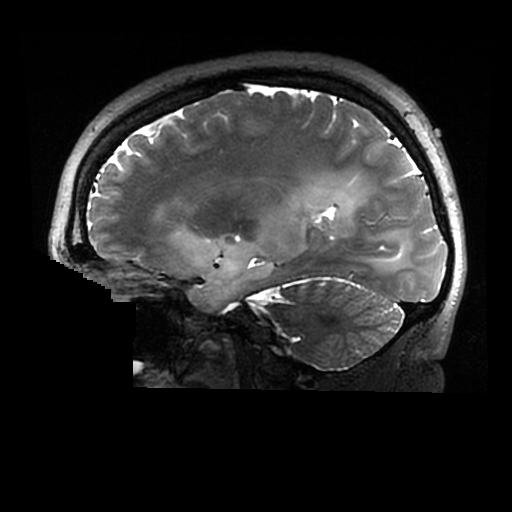
Brain MRI from a brain-tumour surgery series, one sagittal slice; position 185 of 320 along the scan axis; 0.6 mm slice thickness; 512 × 512 image matrix, field of view 240 × 240 mm. Case-level facts recorded for this patient, not image findings: histopathology: Astrocytoma; WHO grade: 2; IDH mutation: yes.
Outlined on this slice (expert manual segmentation):
- tumour: bounding box (x1, y1, x2, y2) in pixels: (173, 180, 407, 310)